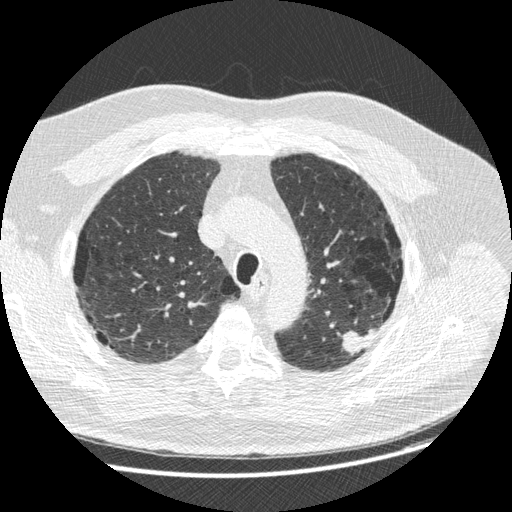
Low-dose screening chest CT, one axial slice. Slice 201 of 258 in the series (ordered by position). Lung window (W 1500 / L -600 HU). 512 × 512 image matrix, field of view 370 × 370 mm.
Annotated regions visible in this slice (outlined manually by an expert reader):
- lesion 1 (tumor, upper lobe of left lung): bounding box (x1, y1, x2, y2) in pixels: (341, 329, 378, 355)